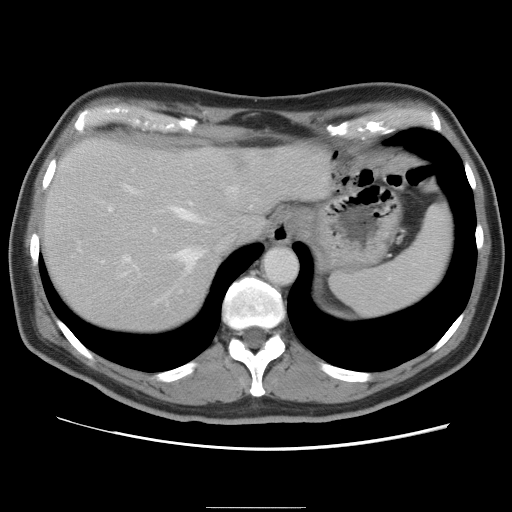
Contrast-enhanced abdominal CT, one axial slice. Slice 66 of 87 in the series (ordered by position). Intravenous contrast given. Soft-tissue window (W 400 / L 40 HU). 5 mm slice thickness. 512 × 512 image matrix. Male patient, age 63 years. Case-level facts recorded for this patient, not image findings: diagnosis: colorectal cancer liver metastases, imaged before liver resection; multiple liver metastases: no; largest metastasis: 9 cm; disease in both lobes: no.
Annotated regions visible in this slice (manually delineated by an expert):
- hepatic veins: bounding box <101,184,238,274> (left, top, right, bottom; pixels)
- liver: <42,139,330,333>
- planned liver remnant (the part of the liver to remain after resection): <42,163,217,333>
- portal vein (with intrahepatic branches): <107,204,172,278>
- liver metastasis: <227,156,245,170>